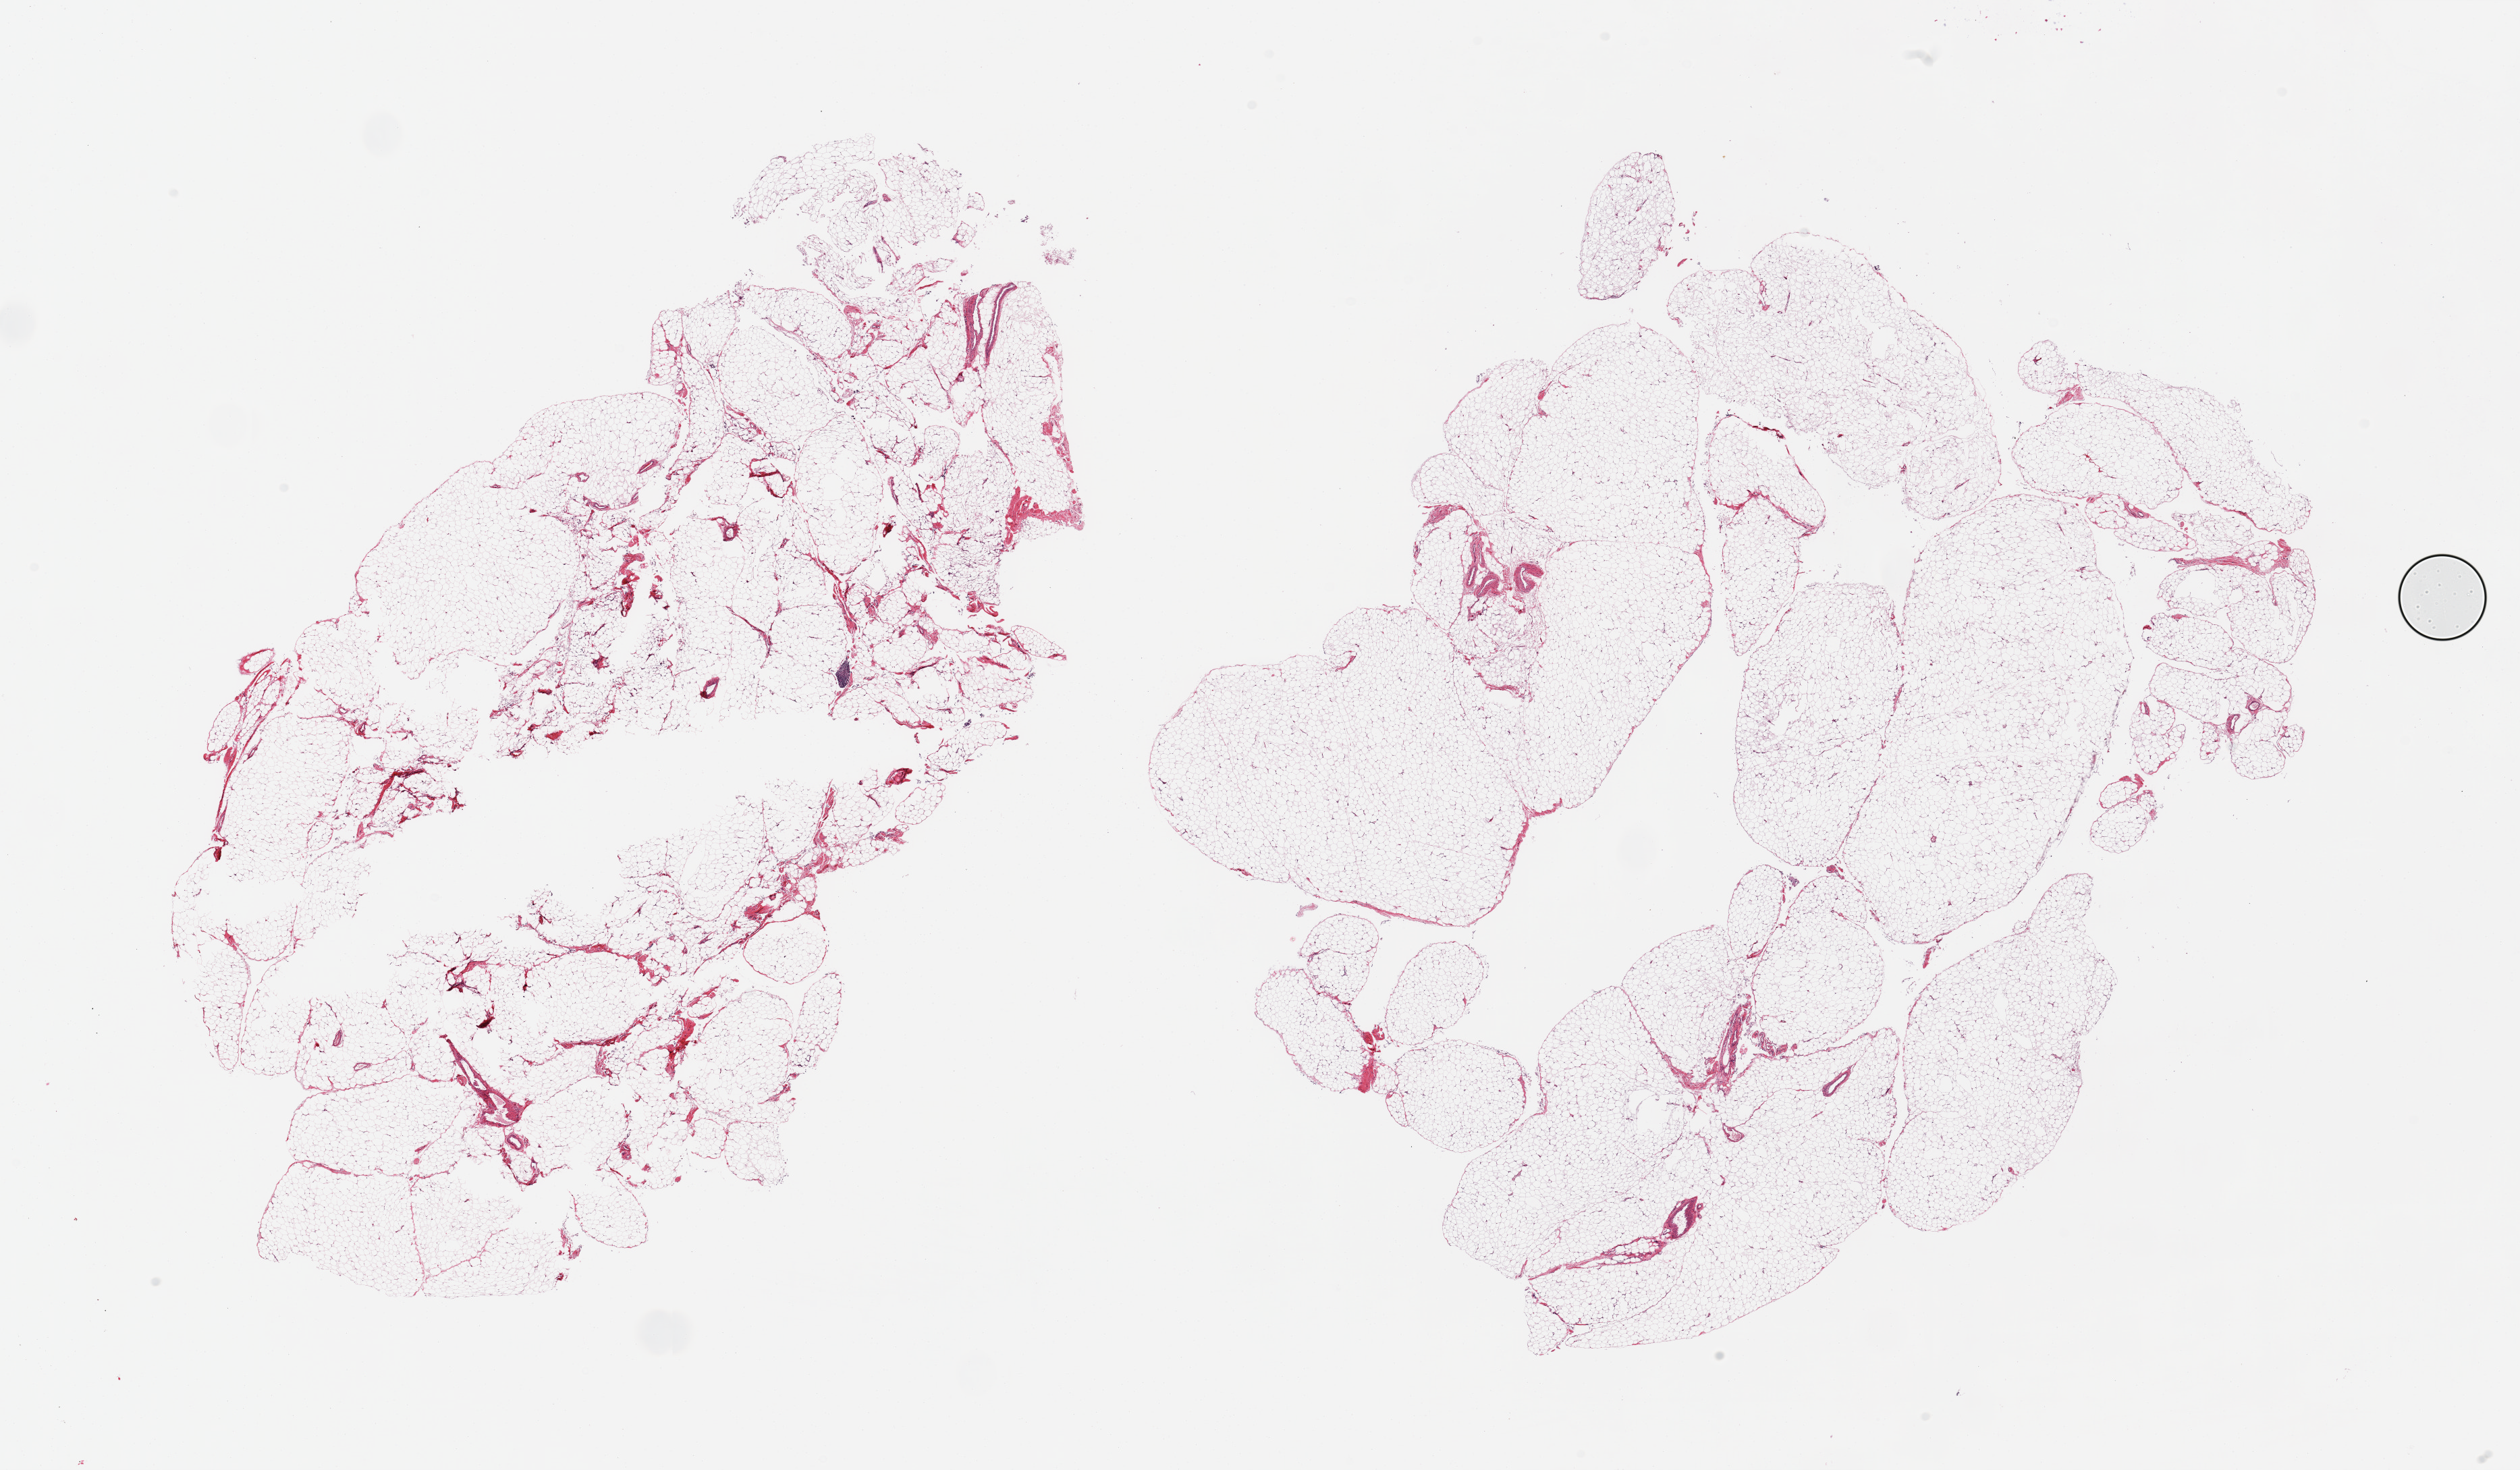
Digitized hematoxylin and eosin (H&E)-stained section, brightfield — whole scanned area (about 29.5 x 17.2 mm) shown as a low-resolution overview; PAXgene-fixed paraffin-embedded (PFPE) section; sampled site (target tissue): omentum; donor tissue sample. Donor sex: female.
Pathologist's review note for this sample: 2 pieces; adipose tissue, central defect in 1 piece.